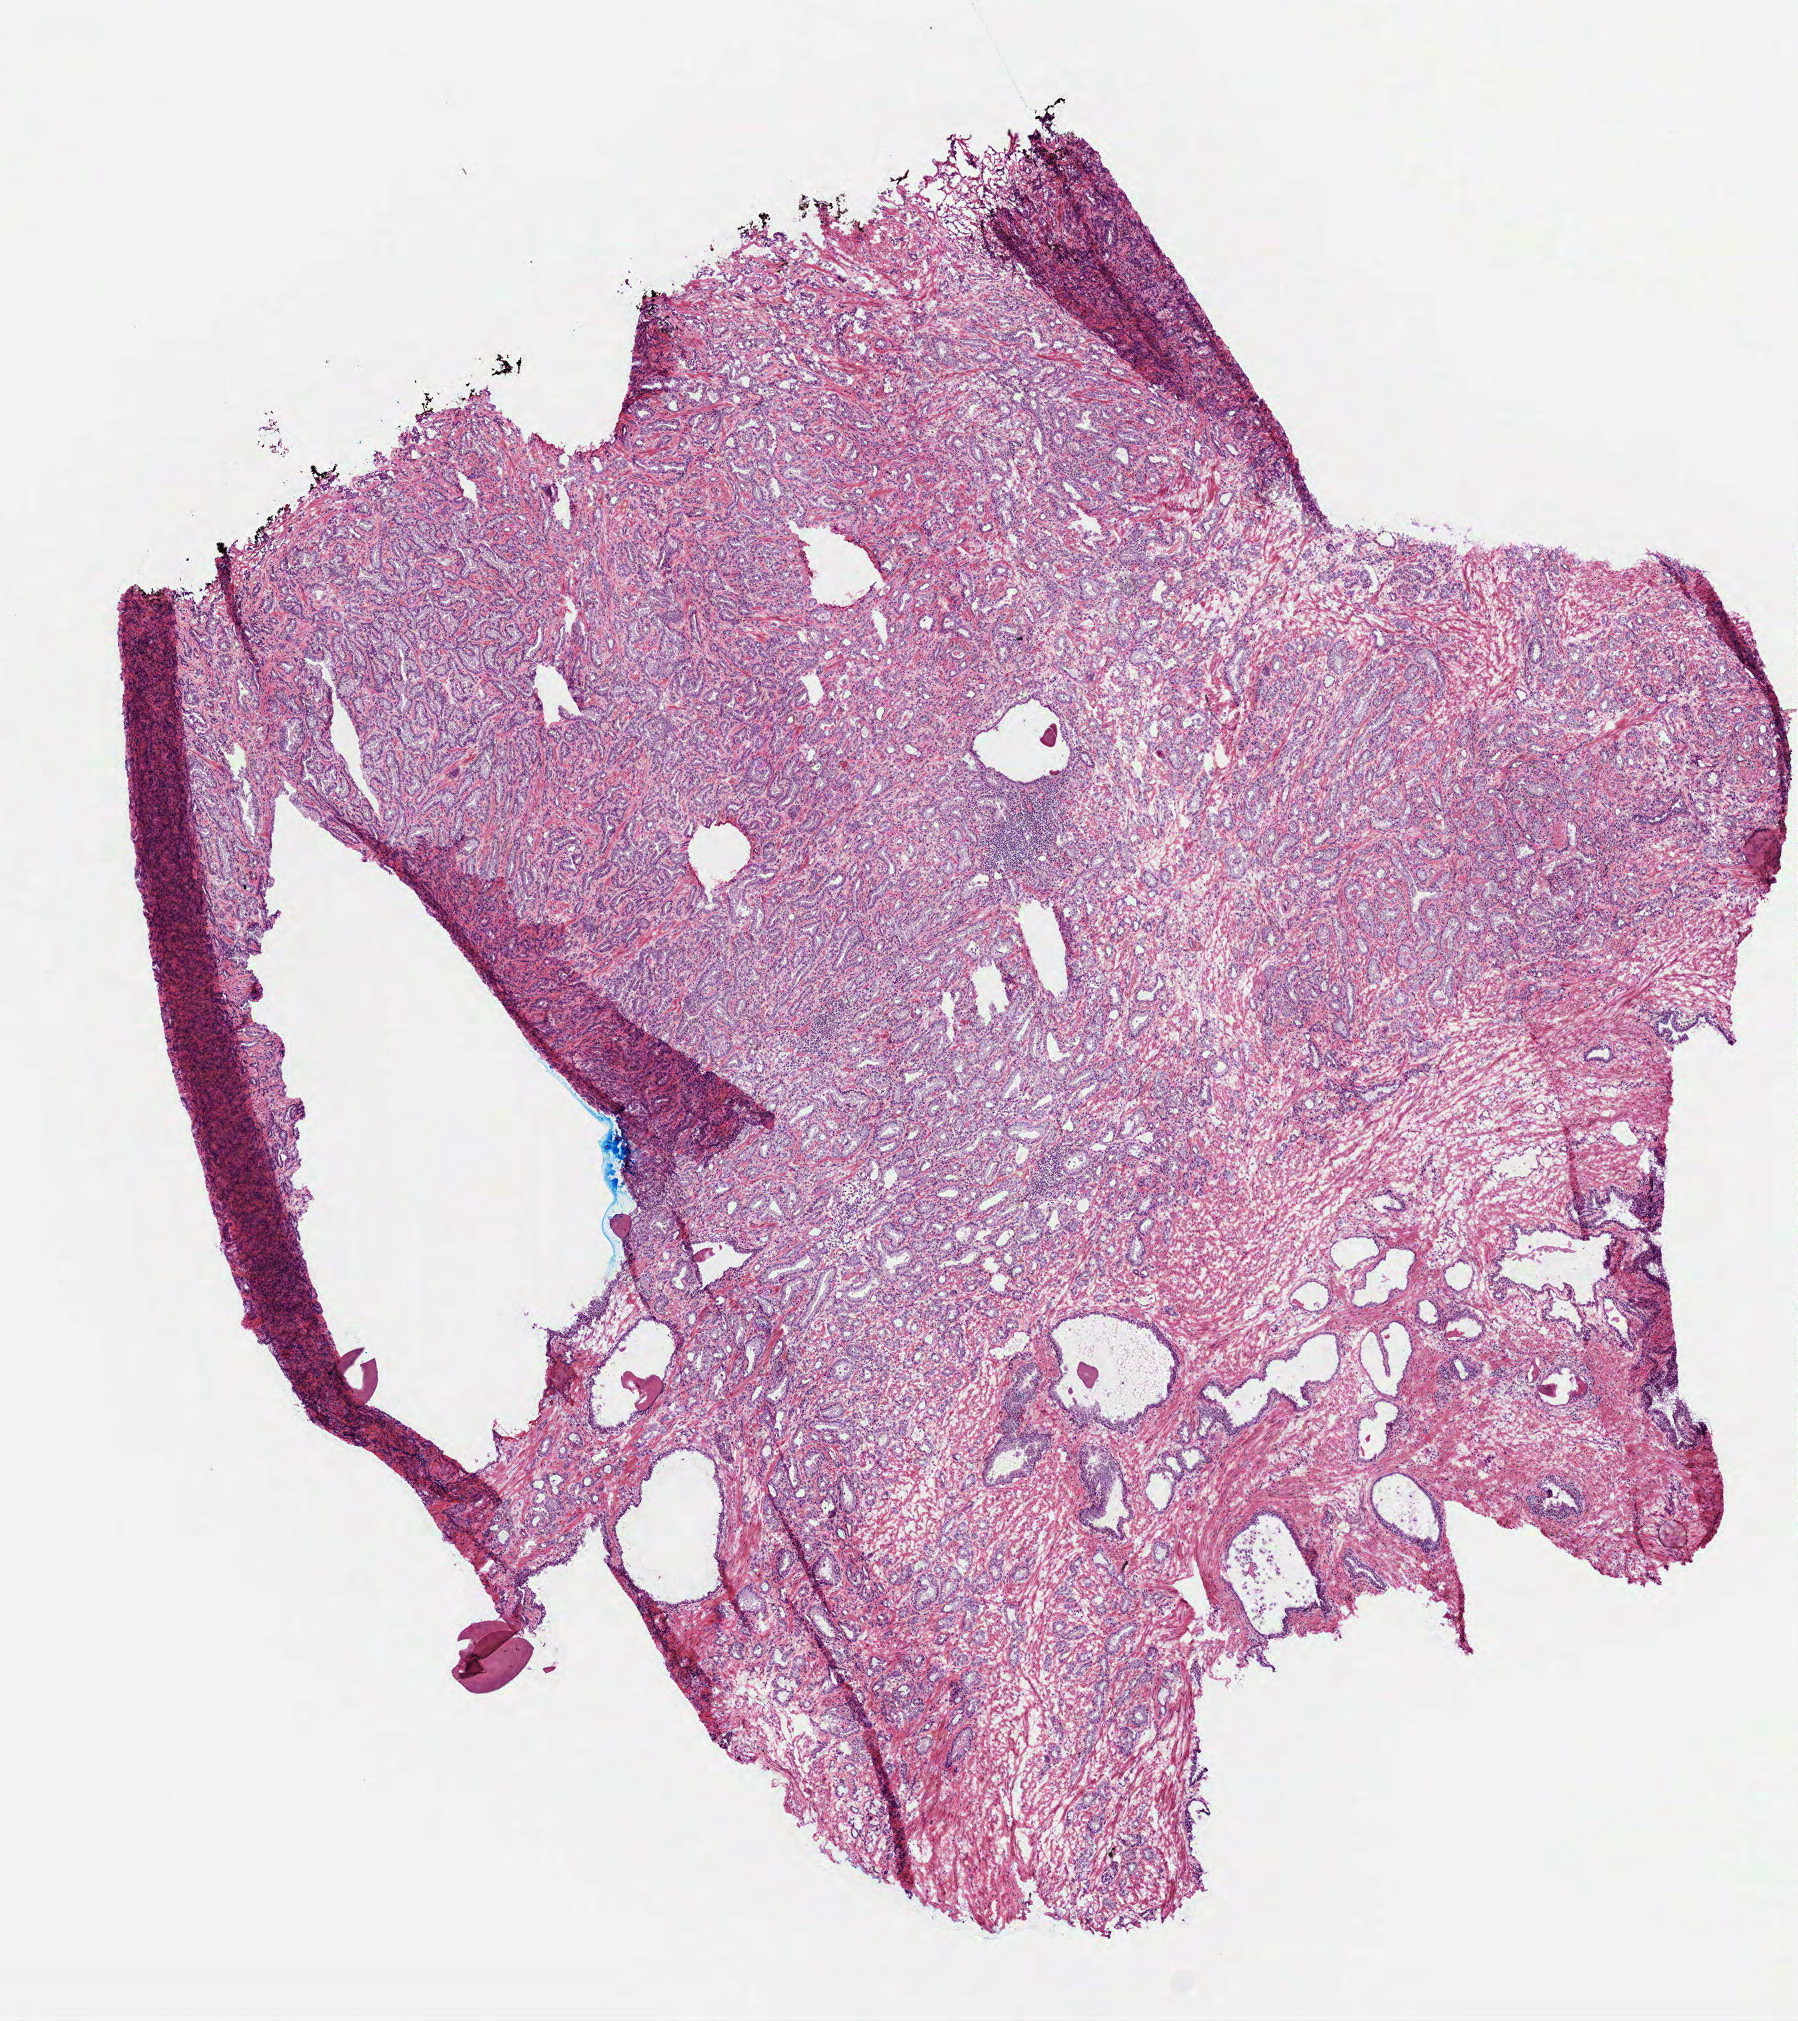
H&E-stained whole-slide image — shown as a low-resolution overview of the whole scanned area (about 7.3 x 8.2 mm, acquisition: 40x scan). Frozen section. Primary tumour sample from the prostate. Male, age 73 years at initial diagnosis. Gleason score: 7 (4+3).
* histologic diagnosis: Acinar cell carcinoma (prostate gland)